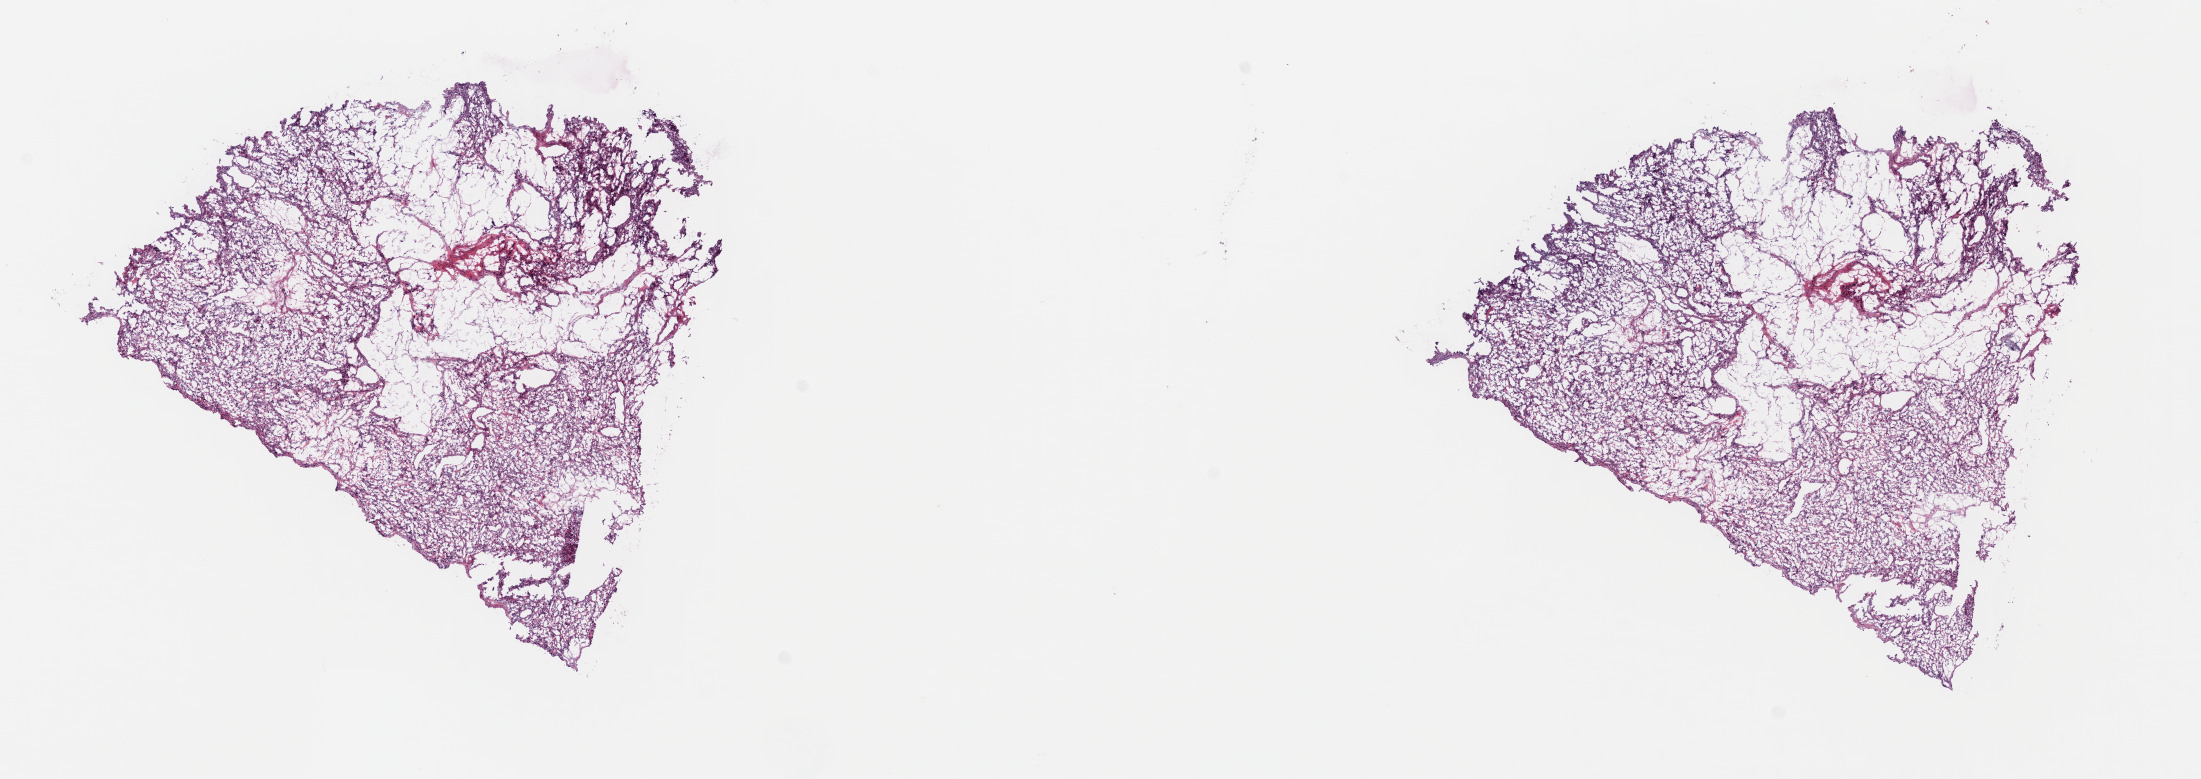
H&E-stained whole-slide image, a low-resolution overview of the entire scanned area, about 17.3 x 6.1 mm; frozen section; primary tumour sample from the adrenal gland. Female, age 35 years at initial diagnosis. Slide review estimates, as recorded: tumour cells 70%, tumour nuclei 75%, normal cells 0%, stromal cells 30%, necrosis 0%. Infiltration values recorded for this section: lymphocyte infiltration 0%, monocyte infiltration 0%, neutrophil infiltration 0%.
- diagnosis: Carcinoid tumor, NOS (pancreas, NOS)
- AJCC pathologic stage: IIA